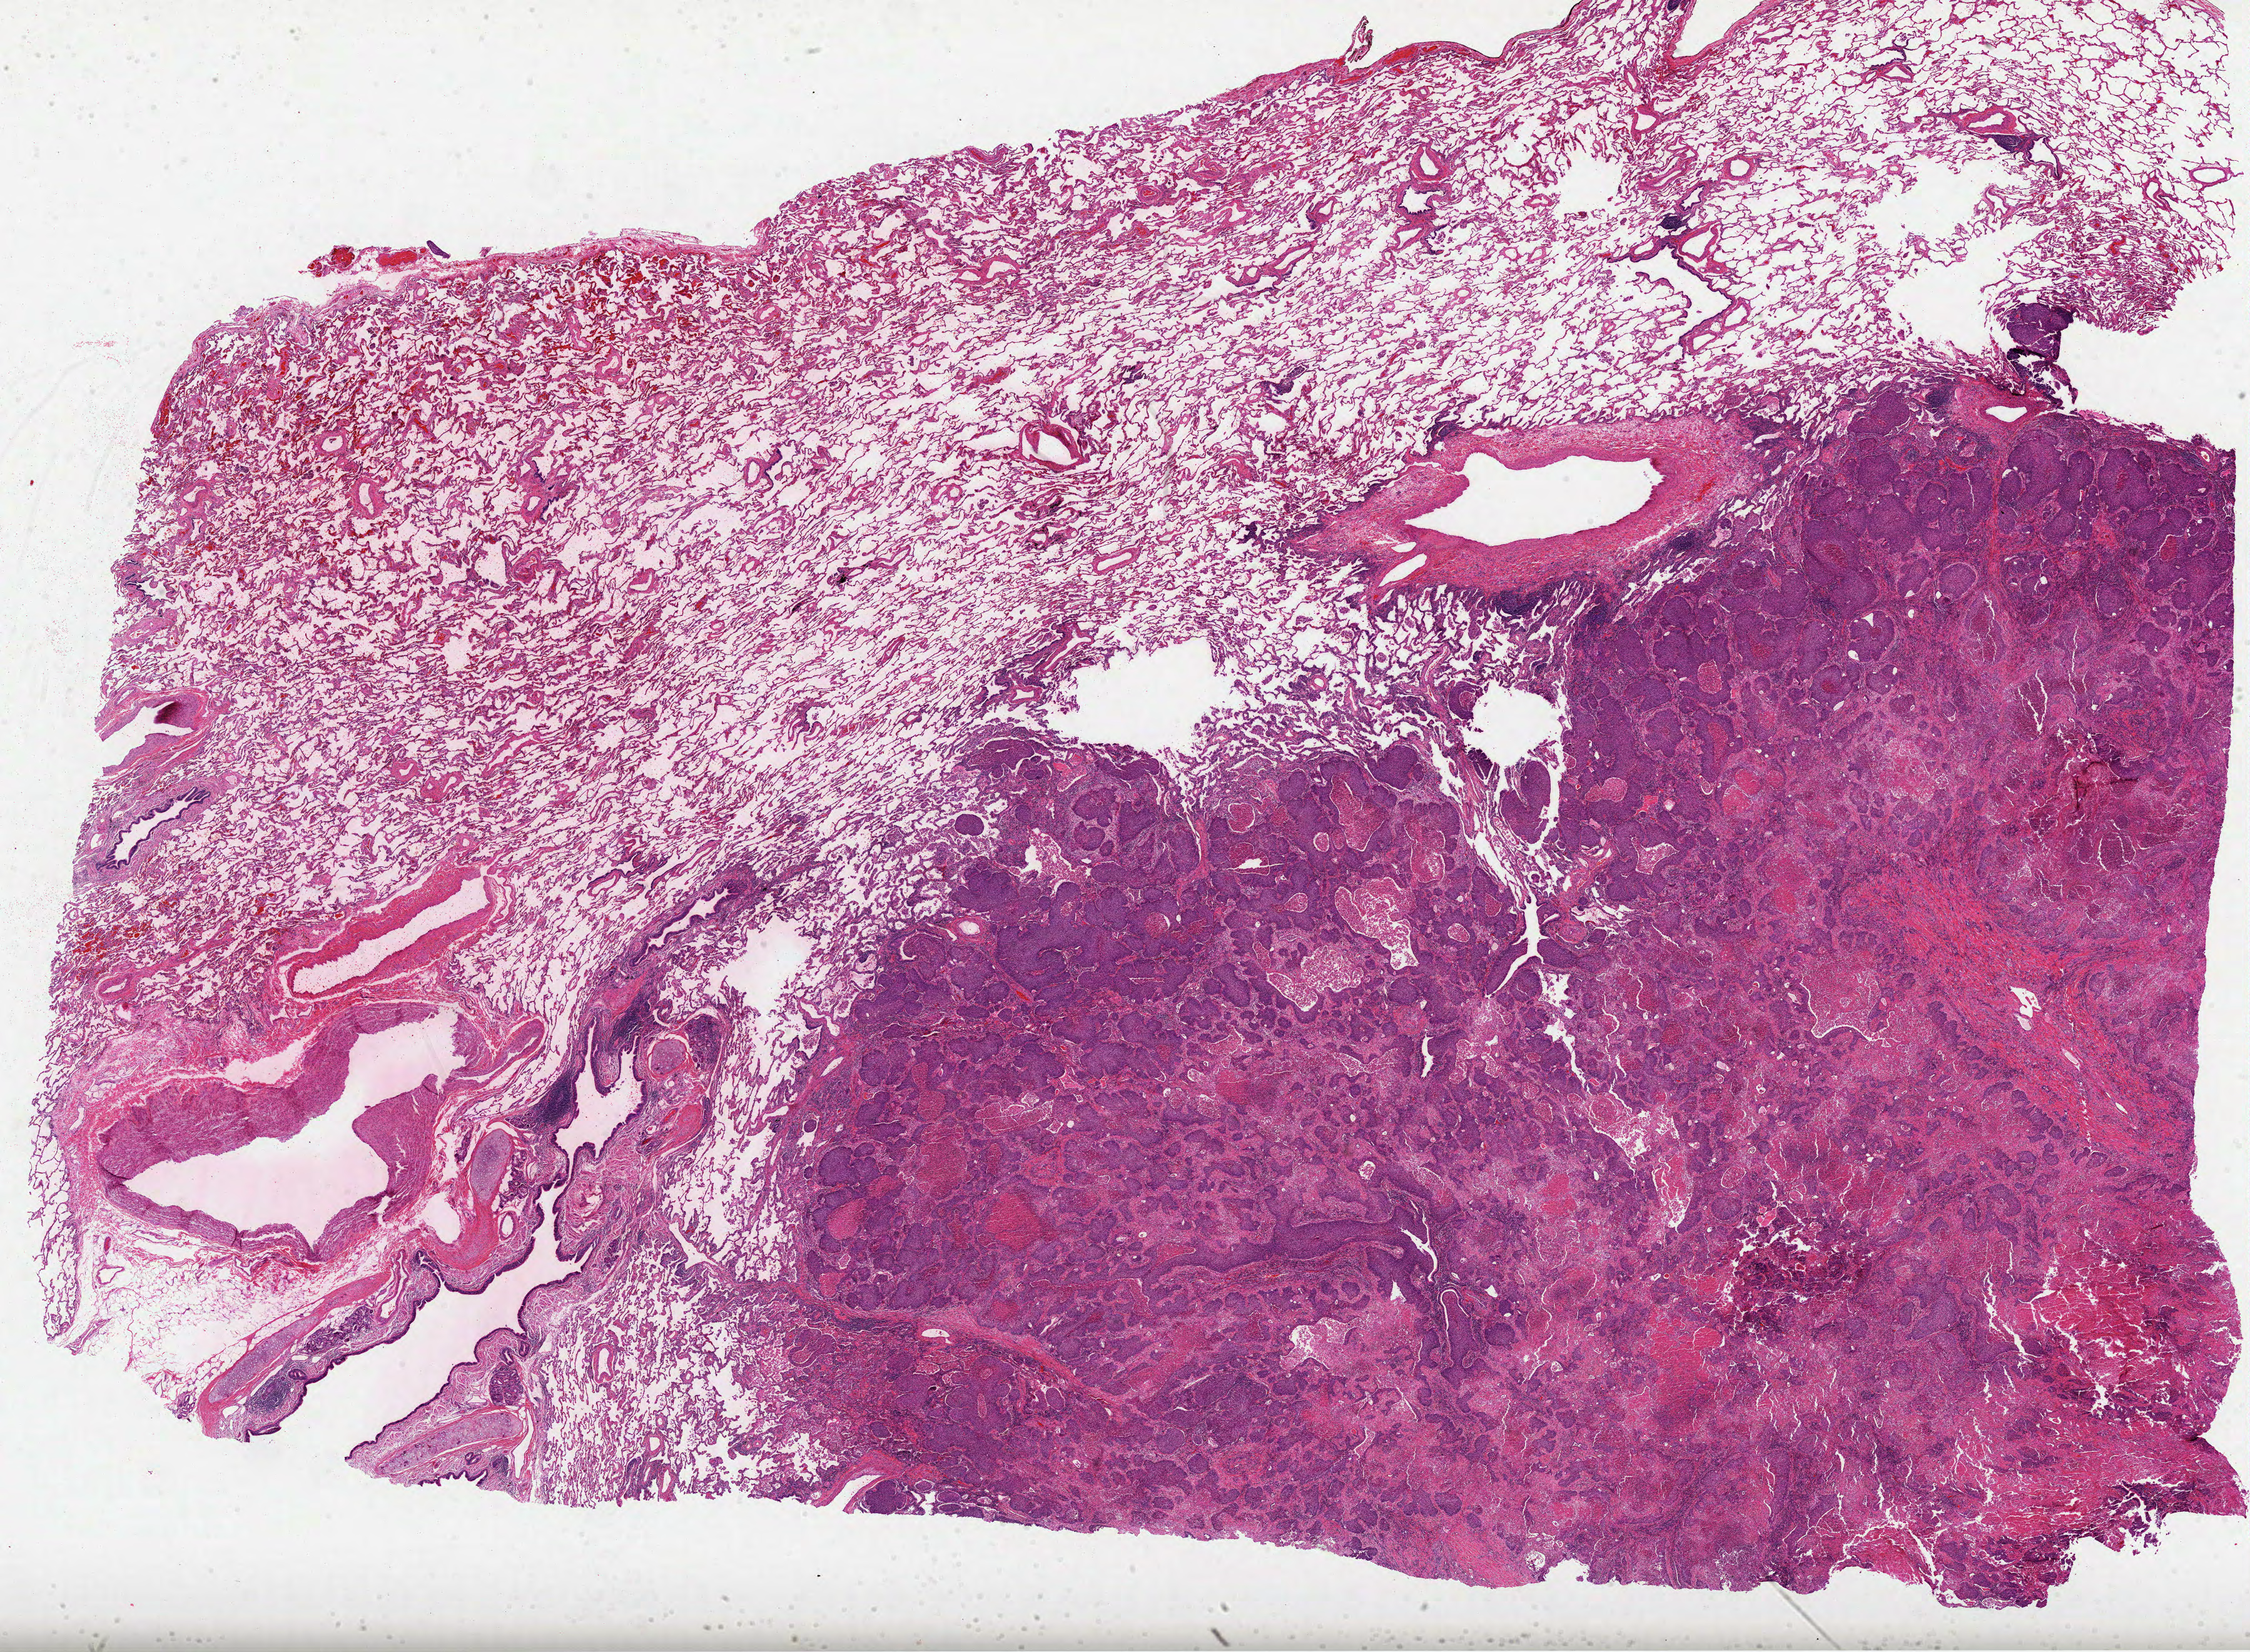
Whole-slide histology image, H&E — shown as a low-resolution overview of the whole scanned area (about 29.0 x 21.3 mm); formalin-fixed paraffin-embedded (FFPE) diagnostic section; primary tumour sample from the lung. Patient: male, age at initial diagnosis 68 years.
Laterality: right. Pathologic diagnosis: Squamous cell carcinoma, NOS (upper lobe, lung). AJCC pathologic stage: IB (6th edition).